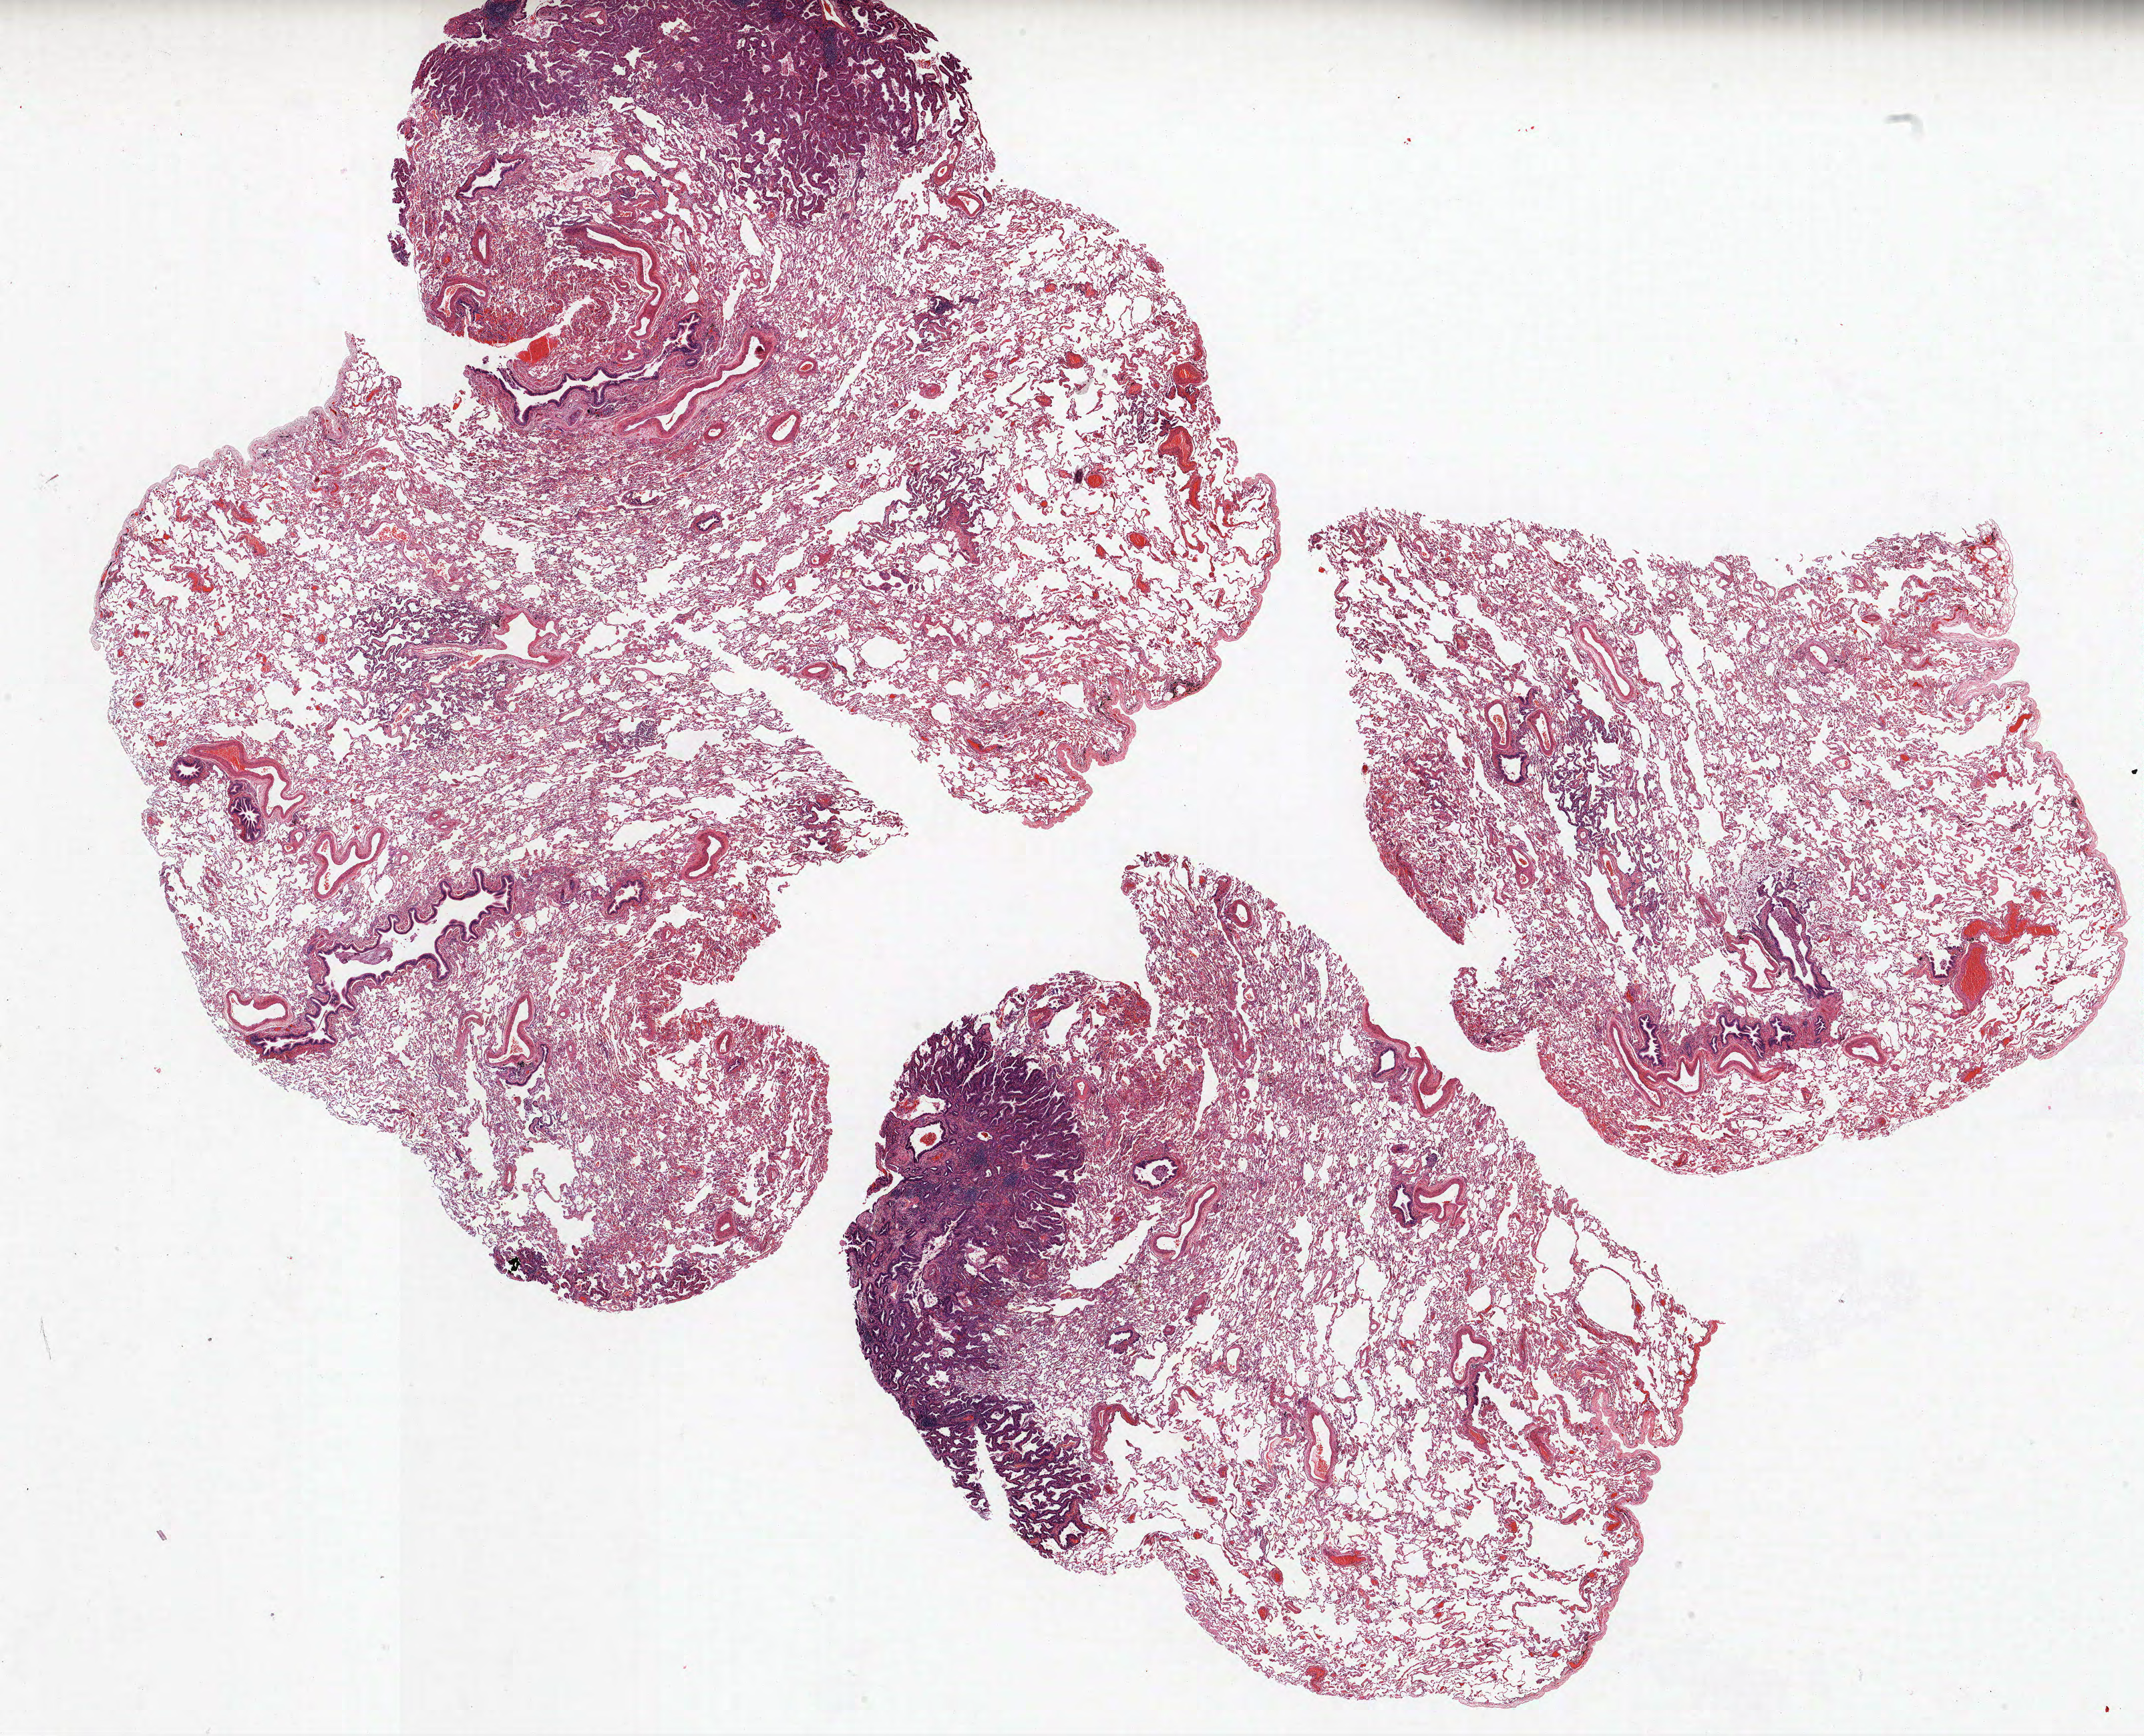
Whole-slide histology image, Hematoxylin and eosin (H&E) stained — a low-resolution overview of the entire scanned area, about 25.7 x 20.8 mm (slide scanned at 40x); formalin-fixed paraffin-embedded (FFPE) section; lung. Female patient, aged 61 at enrolment. Grade: moderately differentiated (G2).
Tumour size (pathology): 30 mm. Stage (AJCC 6th edition): IIA. Primary tumour location (clinical record): right lower lobe. Participant's lung-cancer diagnosis: Adenocarcinoma, NOS. ICD-O-3 topography: lower lobe of lung (C34.3). Note: participant had 2 primary lung cancers recorded; fields above describe the first.